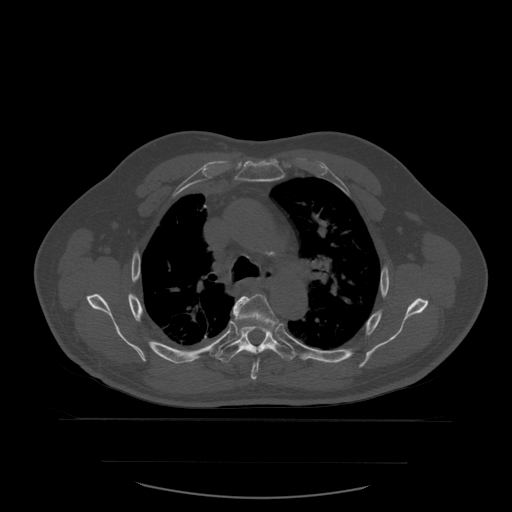
CT including the spine, one axial slice. Slice 414 of 590 in the series (ordered by position). Bone window (W 1800 / L 400 HU). 1.25 mm slice thickness. 512 × 512 image matrix, field of view 479 × 479 mm. Patient age 71 years. Case-level facts recorded for this patient, not image findings: primary cancer: lung; vertebrae with lytic lesions (as recorded): T1, T2, L5, S1.
Outlined on this slice (semi-automatically segmented with operator editing):
- T5 vertebra: box from (x=234, y=294) to (x=278, y=380) px
- T6 vertebra: (x=216, y=308)–(x=295, y=363)